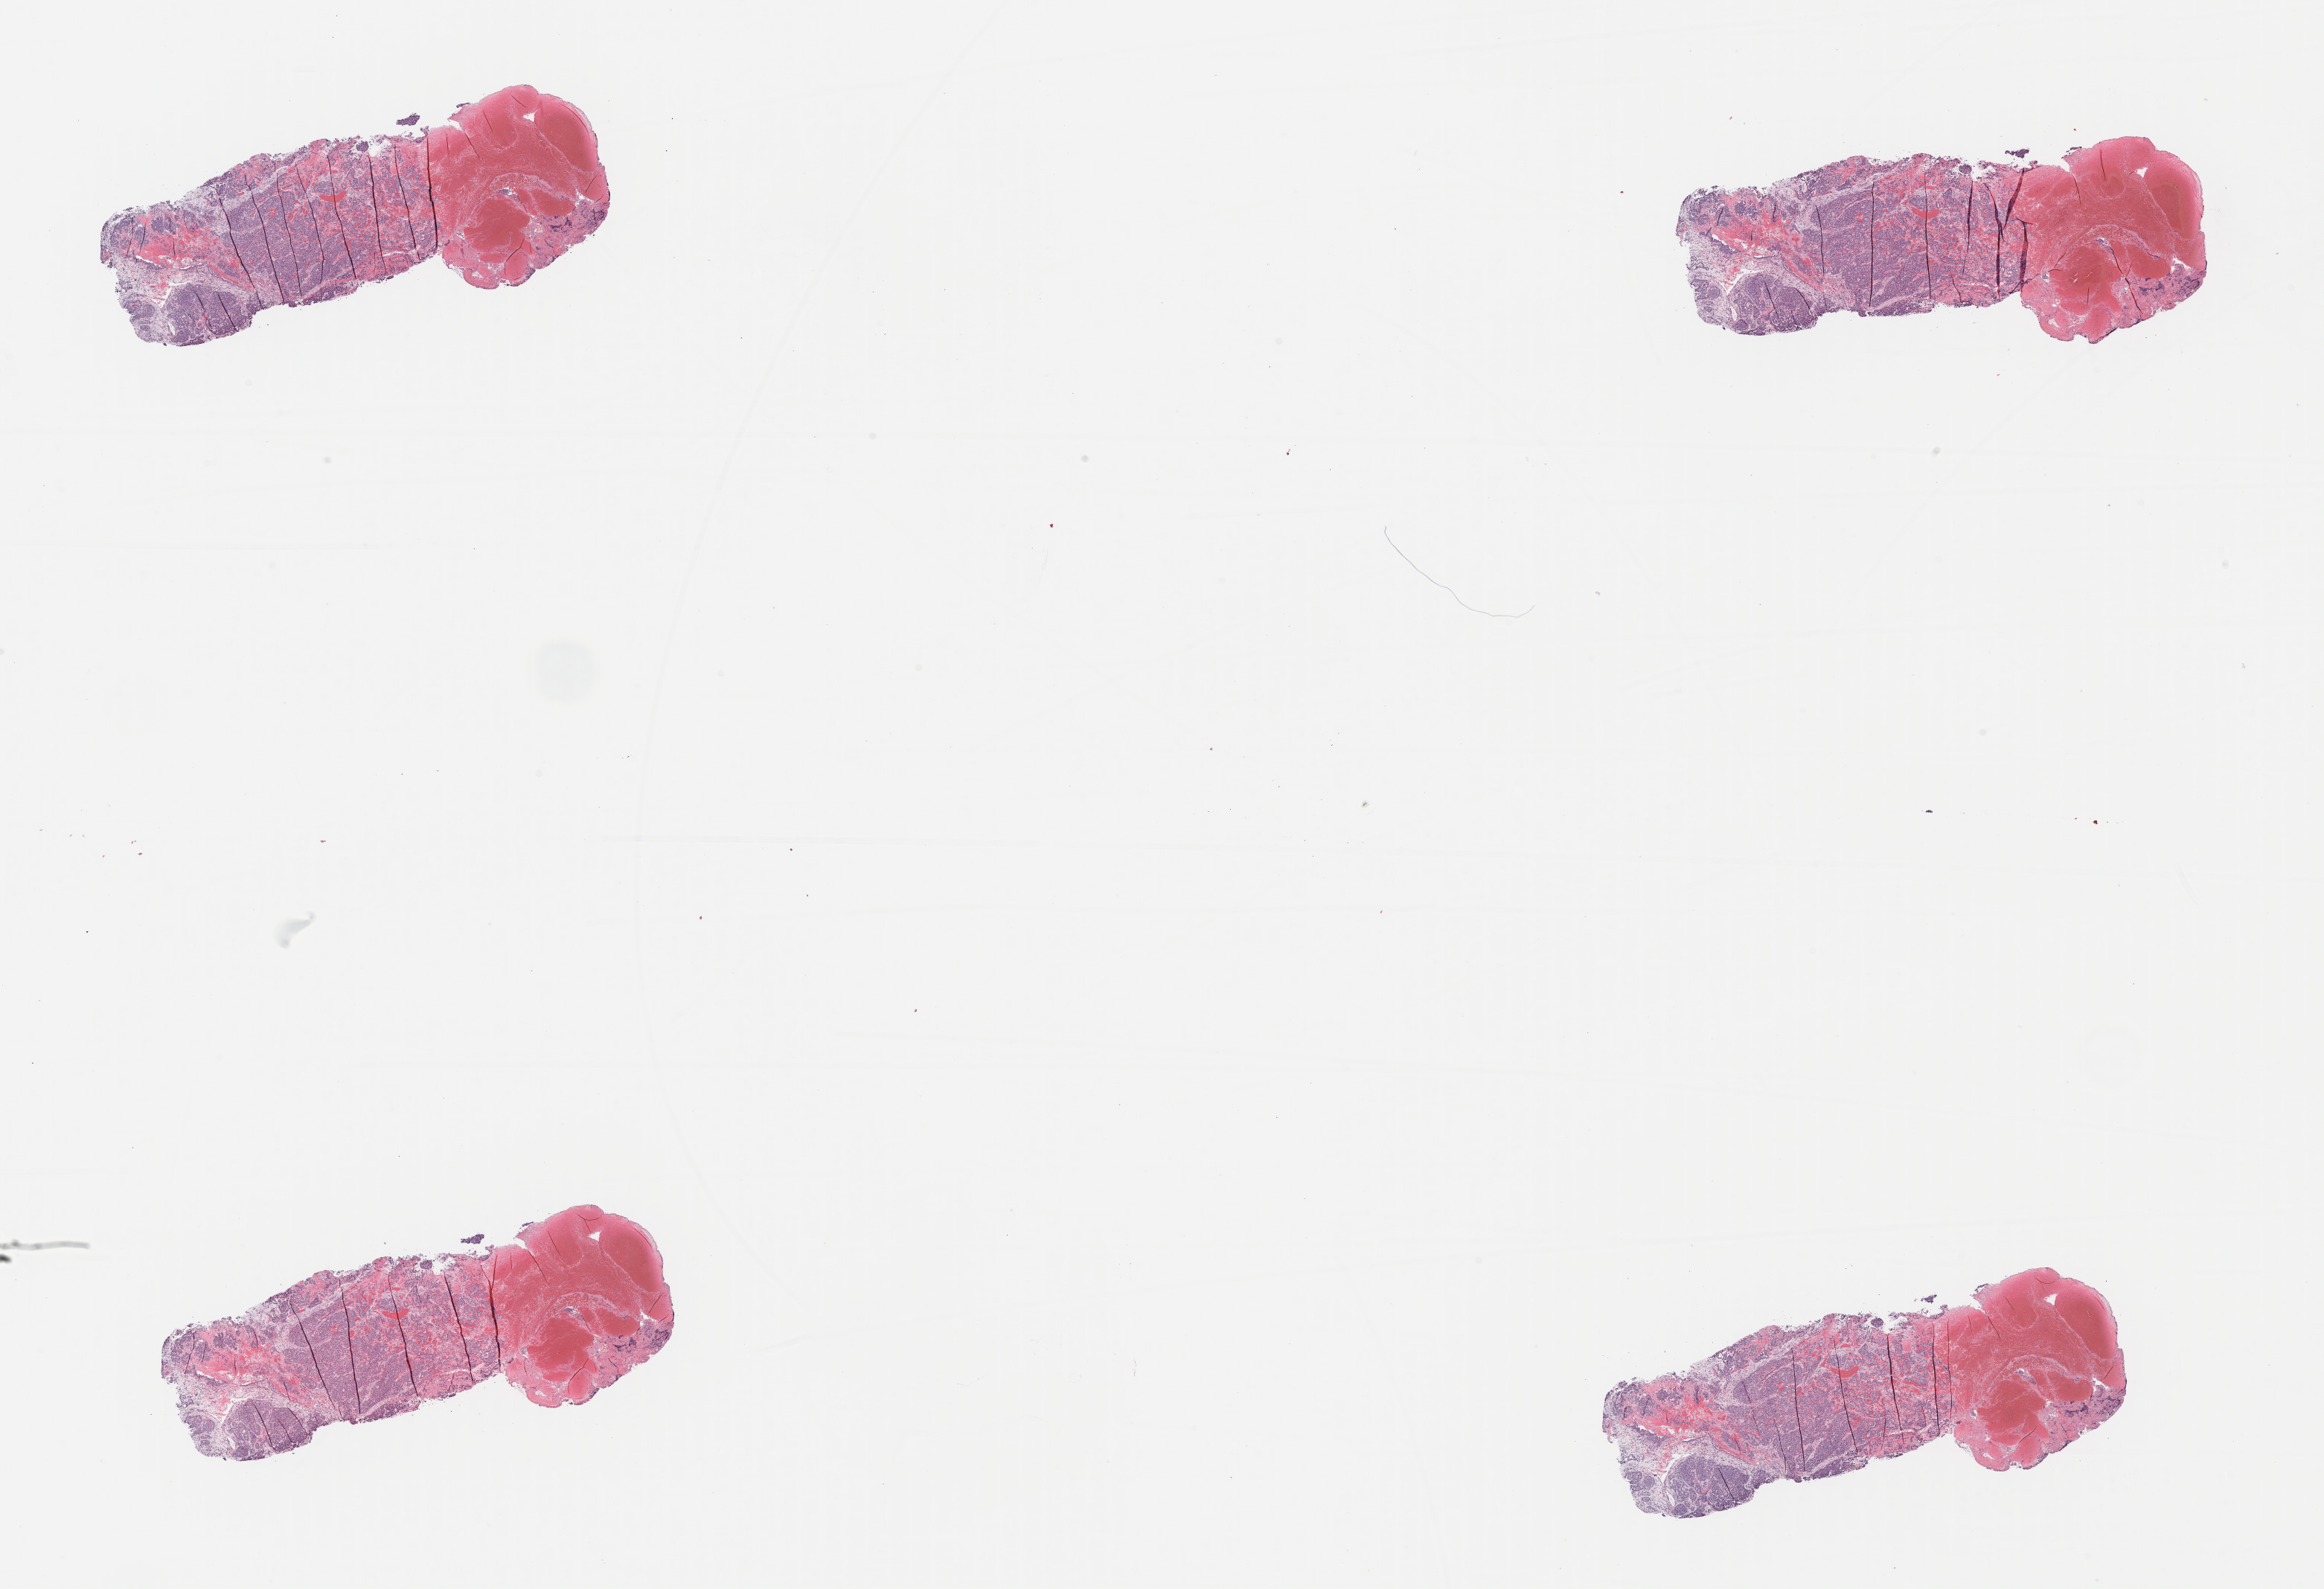
Hematoxylin and eosin (H&E) stained whole-slide image, a low-resolution overview of the entire scanned area, about 24.6 x 16.8 mm; formalin-fixed paraffin-embedded (FFPE) diagnostic section; uterus, primary tumour sample. Female, age 69 years at initial diagnosis.
Histologic diagnosis: Serous cystadenocarcinoma, NOS (endometrium).